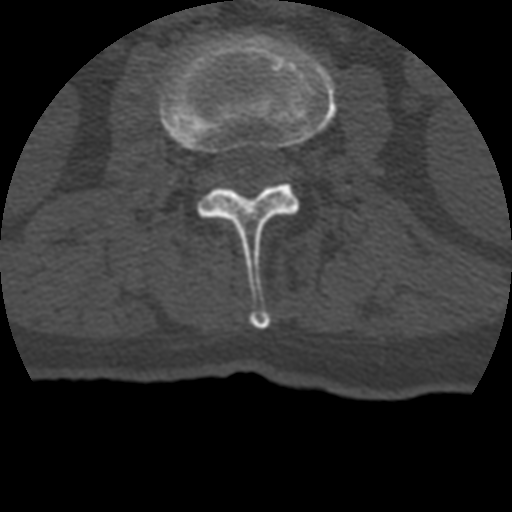
CT including the spine, one axial slice. Position 111 of 399 along the scan axis. Reconstruction kernel STANDARD. 120 kVp. Bone window (W 1800 / L 400 HU). 1.25 mm slice thickness. 512 × 512 image matrix. Patient age 69 years. From the clinical record (not read from this slice): primary cancer: prostate.
Annotated regions visible in this slice (semi-automatic segmentation, software-assisted and operator-edited):
- L2 vertebra: bounding box [x1, y1, x2, y2] px = [159, 32, 336, 329]